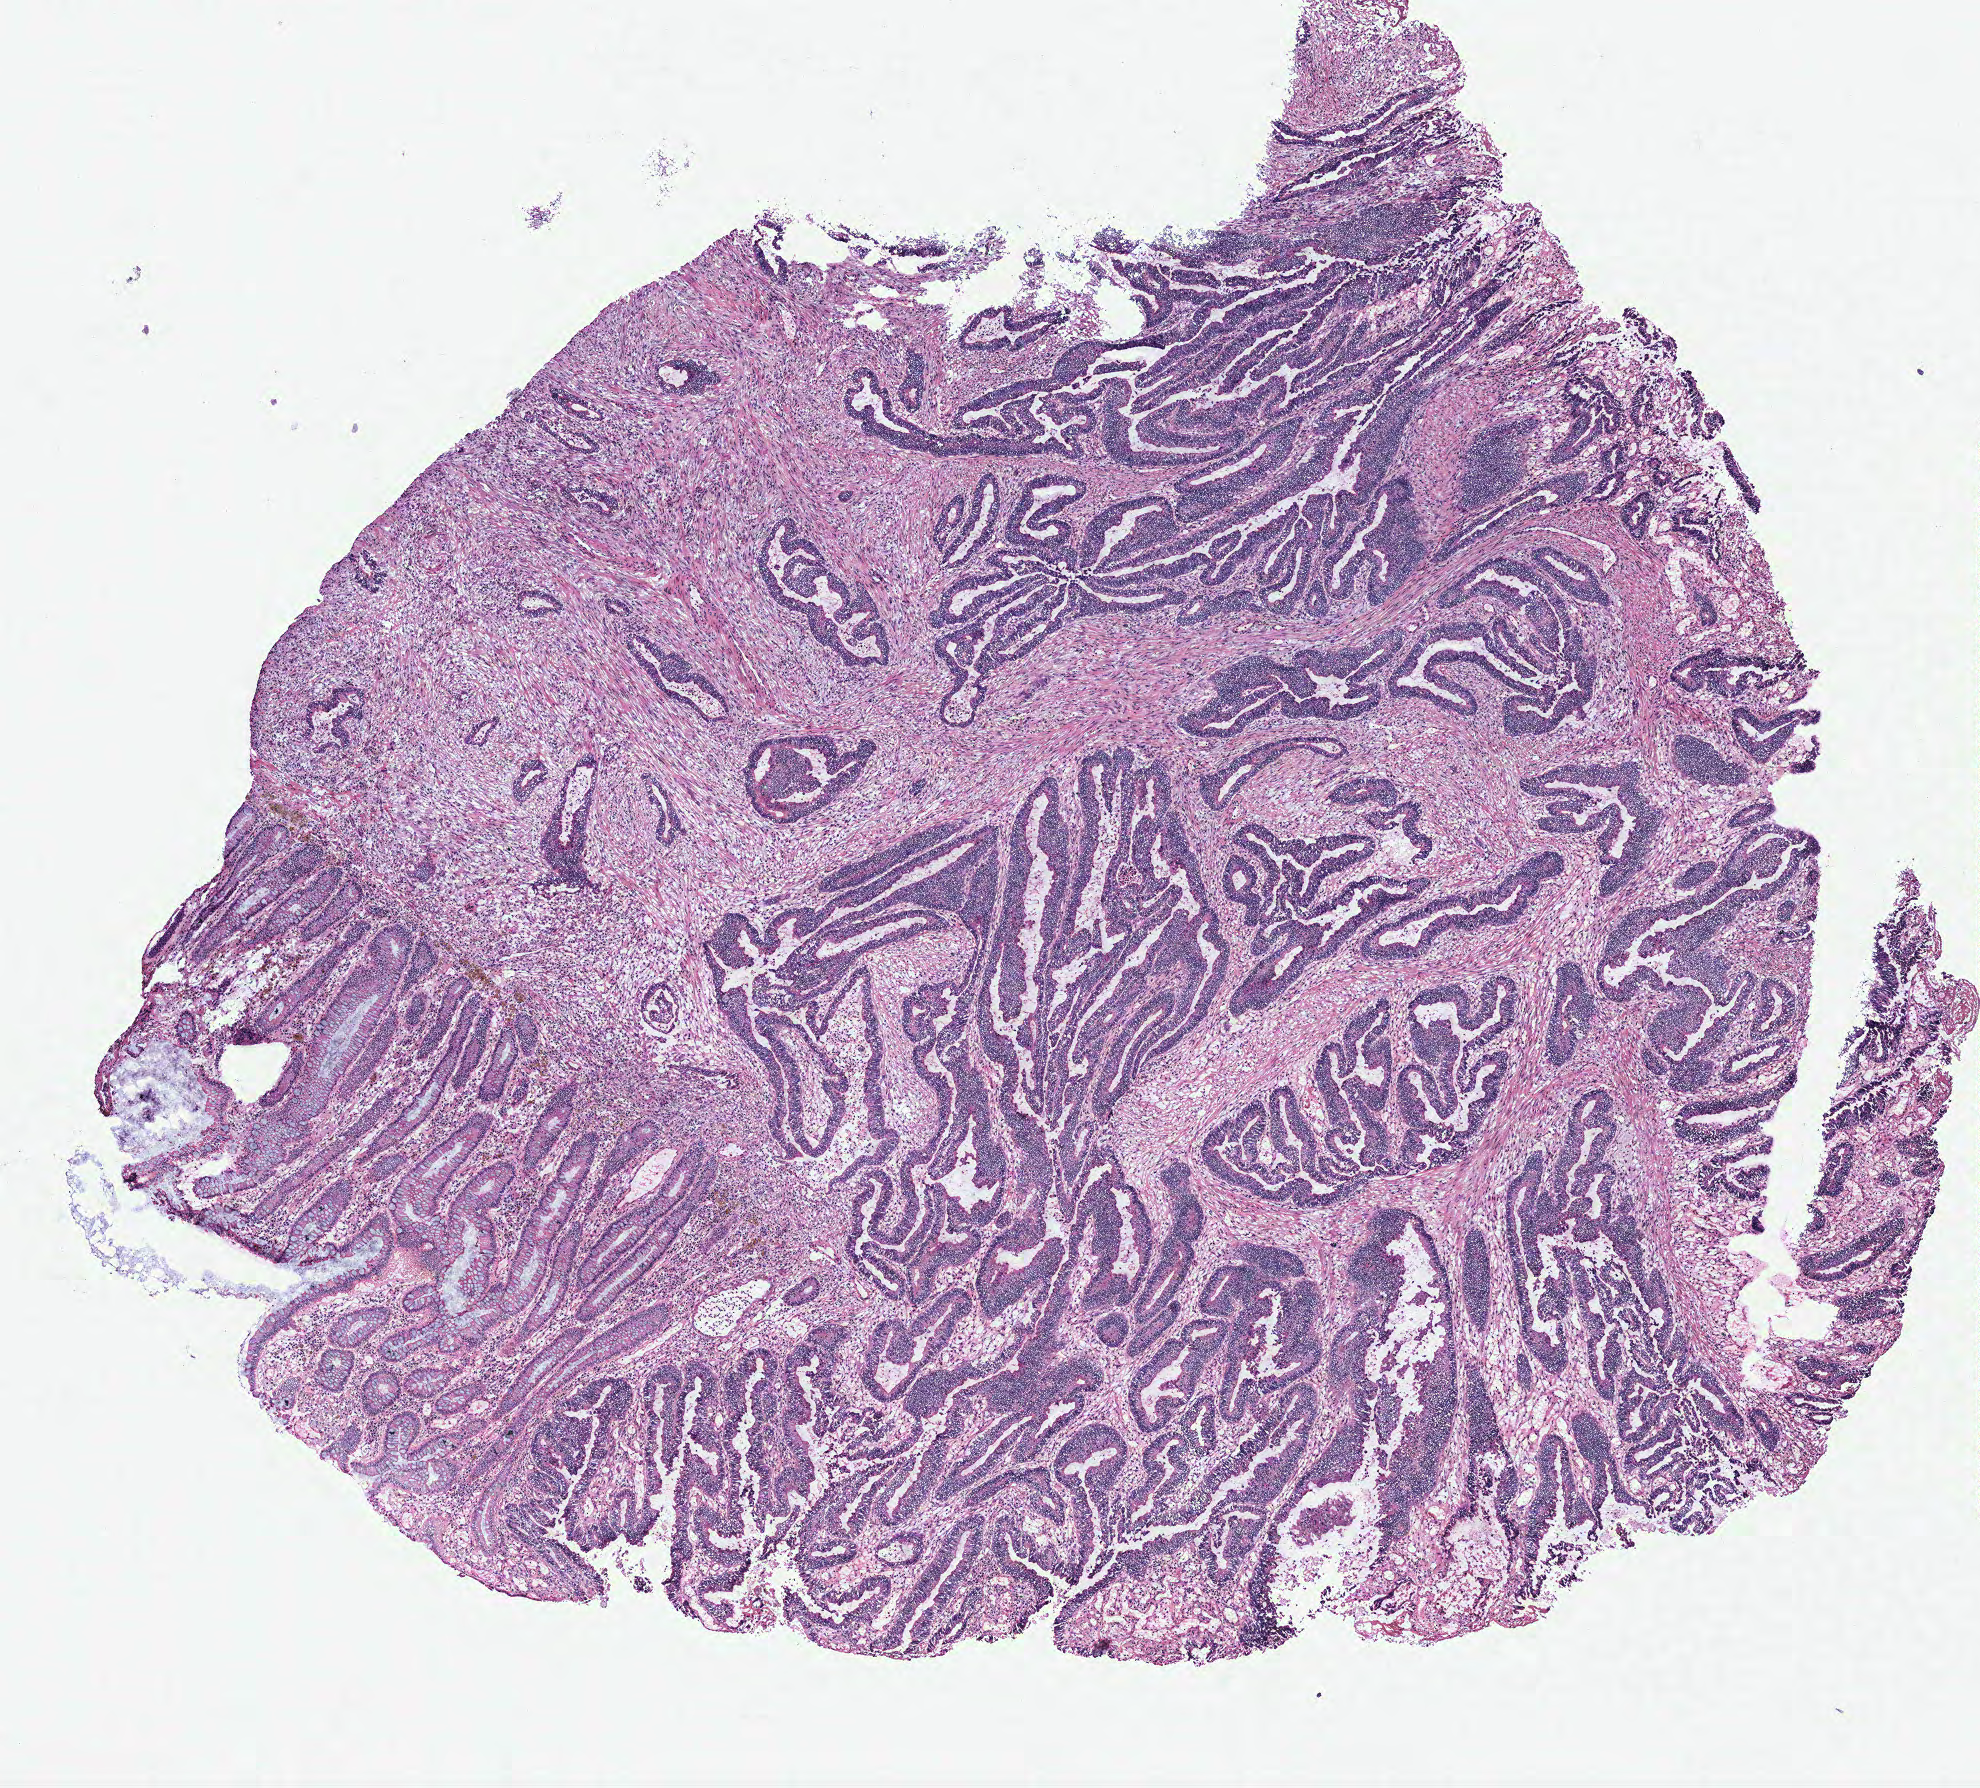
Digitized H&E-stained tissue section (whole slide) — shown as a low-resolution overview of the whole scanned area (about 7.9 x 7.2 mm); colon, normal (non-tumour) tissue. Patient: female, age 70 years.
This section: normal (non-tumour) tissue from the same patient. Patient diagnosis: Adenocarcinoma, NOS.